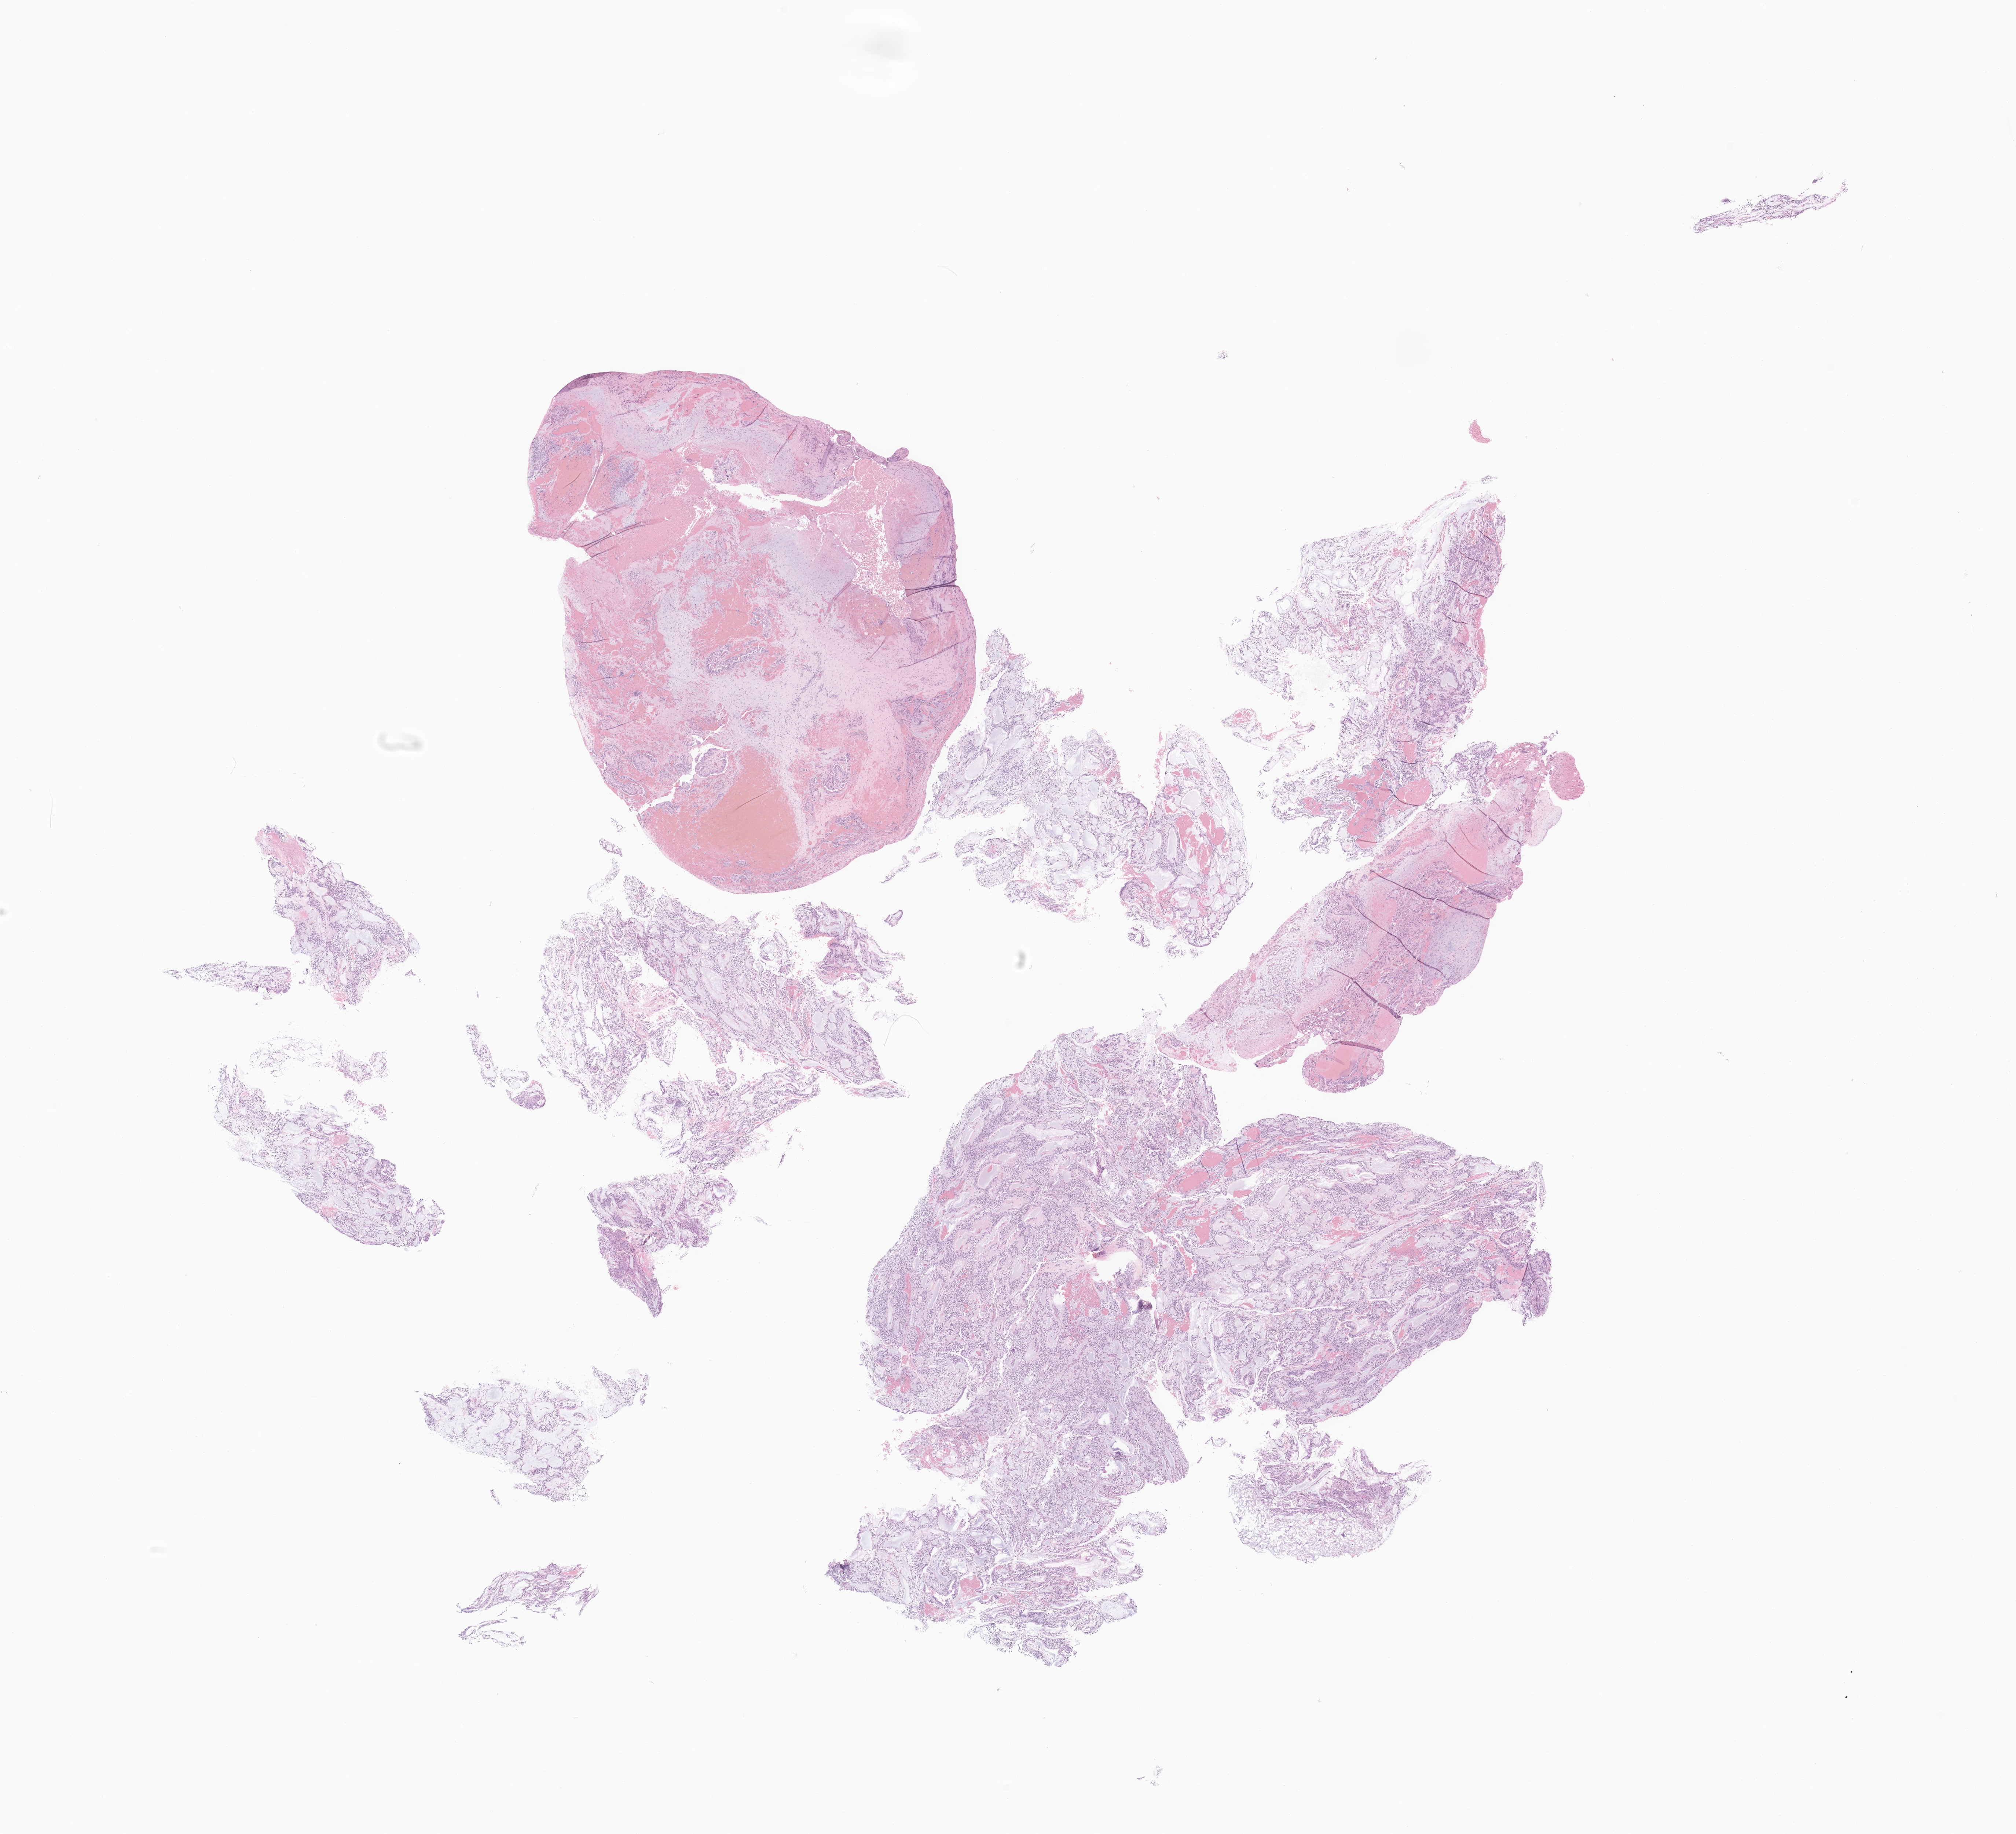
H&E whole-slide image of tumor tissue from the spinal cord — a low-resolution overview of the entire scanned area, about 23.2 x 21.1 mm, formalin-fixed paraffin-embedded section. Patient female; age 183 months.
- recorded diagnosis: Myxopapillary ependymoma